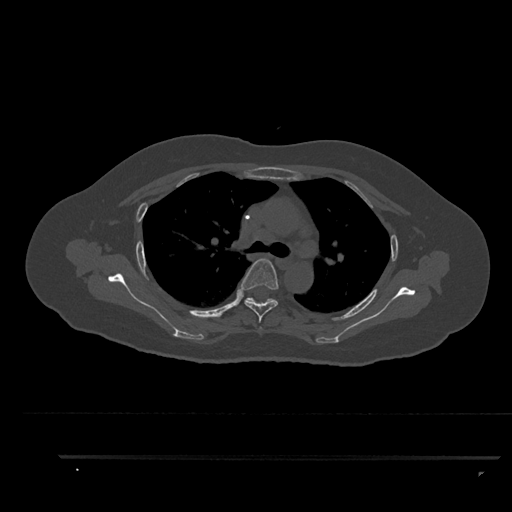
CT including the spine, one axial slice. Position 635 of 797 along the scan axis. Reconstruction kernel Br40s/3. 120 kVp. Bone window (W 1800 / L 400 HU). 0.5 mm slice thickness. 512 × 512 image matrix. Patient: female, 44 years. Case-level facts recorded for this patient, not image findings: primary cancer: renal; vertebrae with lytic lesions (as recorded): L1.
Annotated regions visible in this slice (semi-automatic segmentation, software-assisted and operator-edited):
- T3 vertebra: bounding box <260,326,262,329> (left, top, right, bottom; pixels)
- T4 vertebra: <241,259,278,322>
- T5 vertebra: <244,298,268,302>